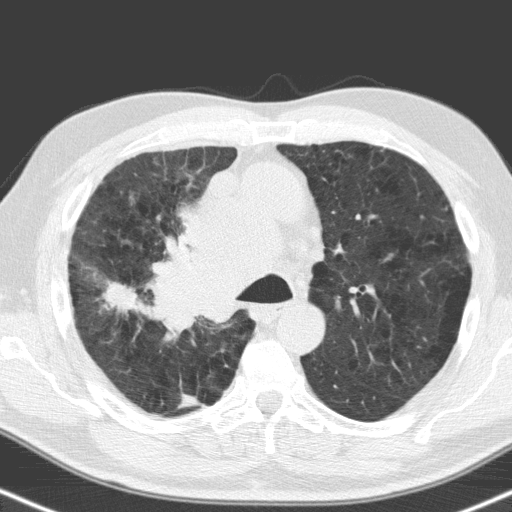
Low-dose screening chest CT, one axial slice; position 113 of 160 along the scan axis; 120 kVp; lung window (W 1500 / L -600 HU); 3.2 mm slice thickness; 512 × 512 image matrix, field of view 324 × 324 mm.
Outlined on this slice (manually delineated by an expert):
- lesion 1 (tumor, hilum of right lung): bounding box <155,171,265,329> (left, top, right, bottom; pixels)
- lesion 2 (tumor, upper lobe of right lung): <108,281,137,312>